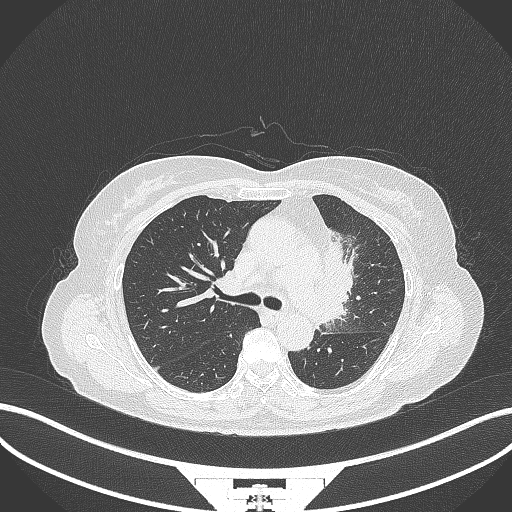
Chest CT, one axial slice; position 214 of 382 along the scan axis; reconstruction kernel B70f; lung window (W 1500 / L -600 HU); 1 mm slice thickness; 512 × 512 image matrix, field of view 400 × 400 mm. Patient: female, 64 years. From the clinical record (not read from this slice): clinical TNM (as recorded): T2a N2 M0.
Structures marked on this image (rectangle marked by the reading radiologist):
- lung tumour (recorded histology: adenocarcinoma): bounding box [x1, y1, x2, y2] px = [322, 231, 357, 324]